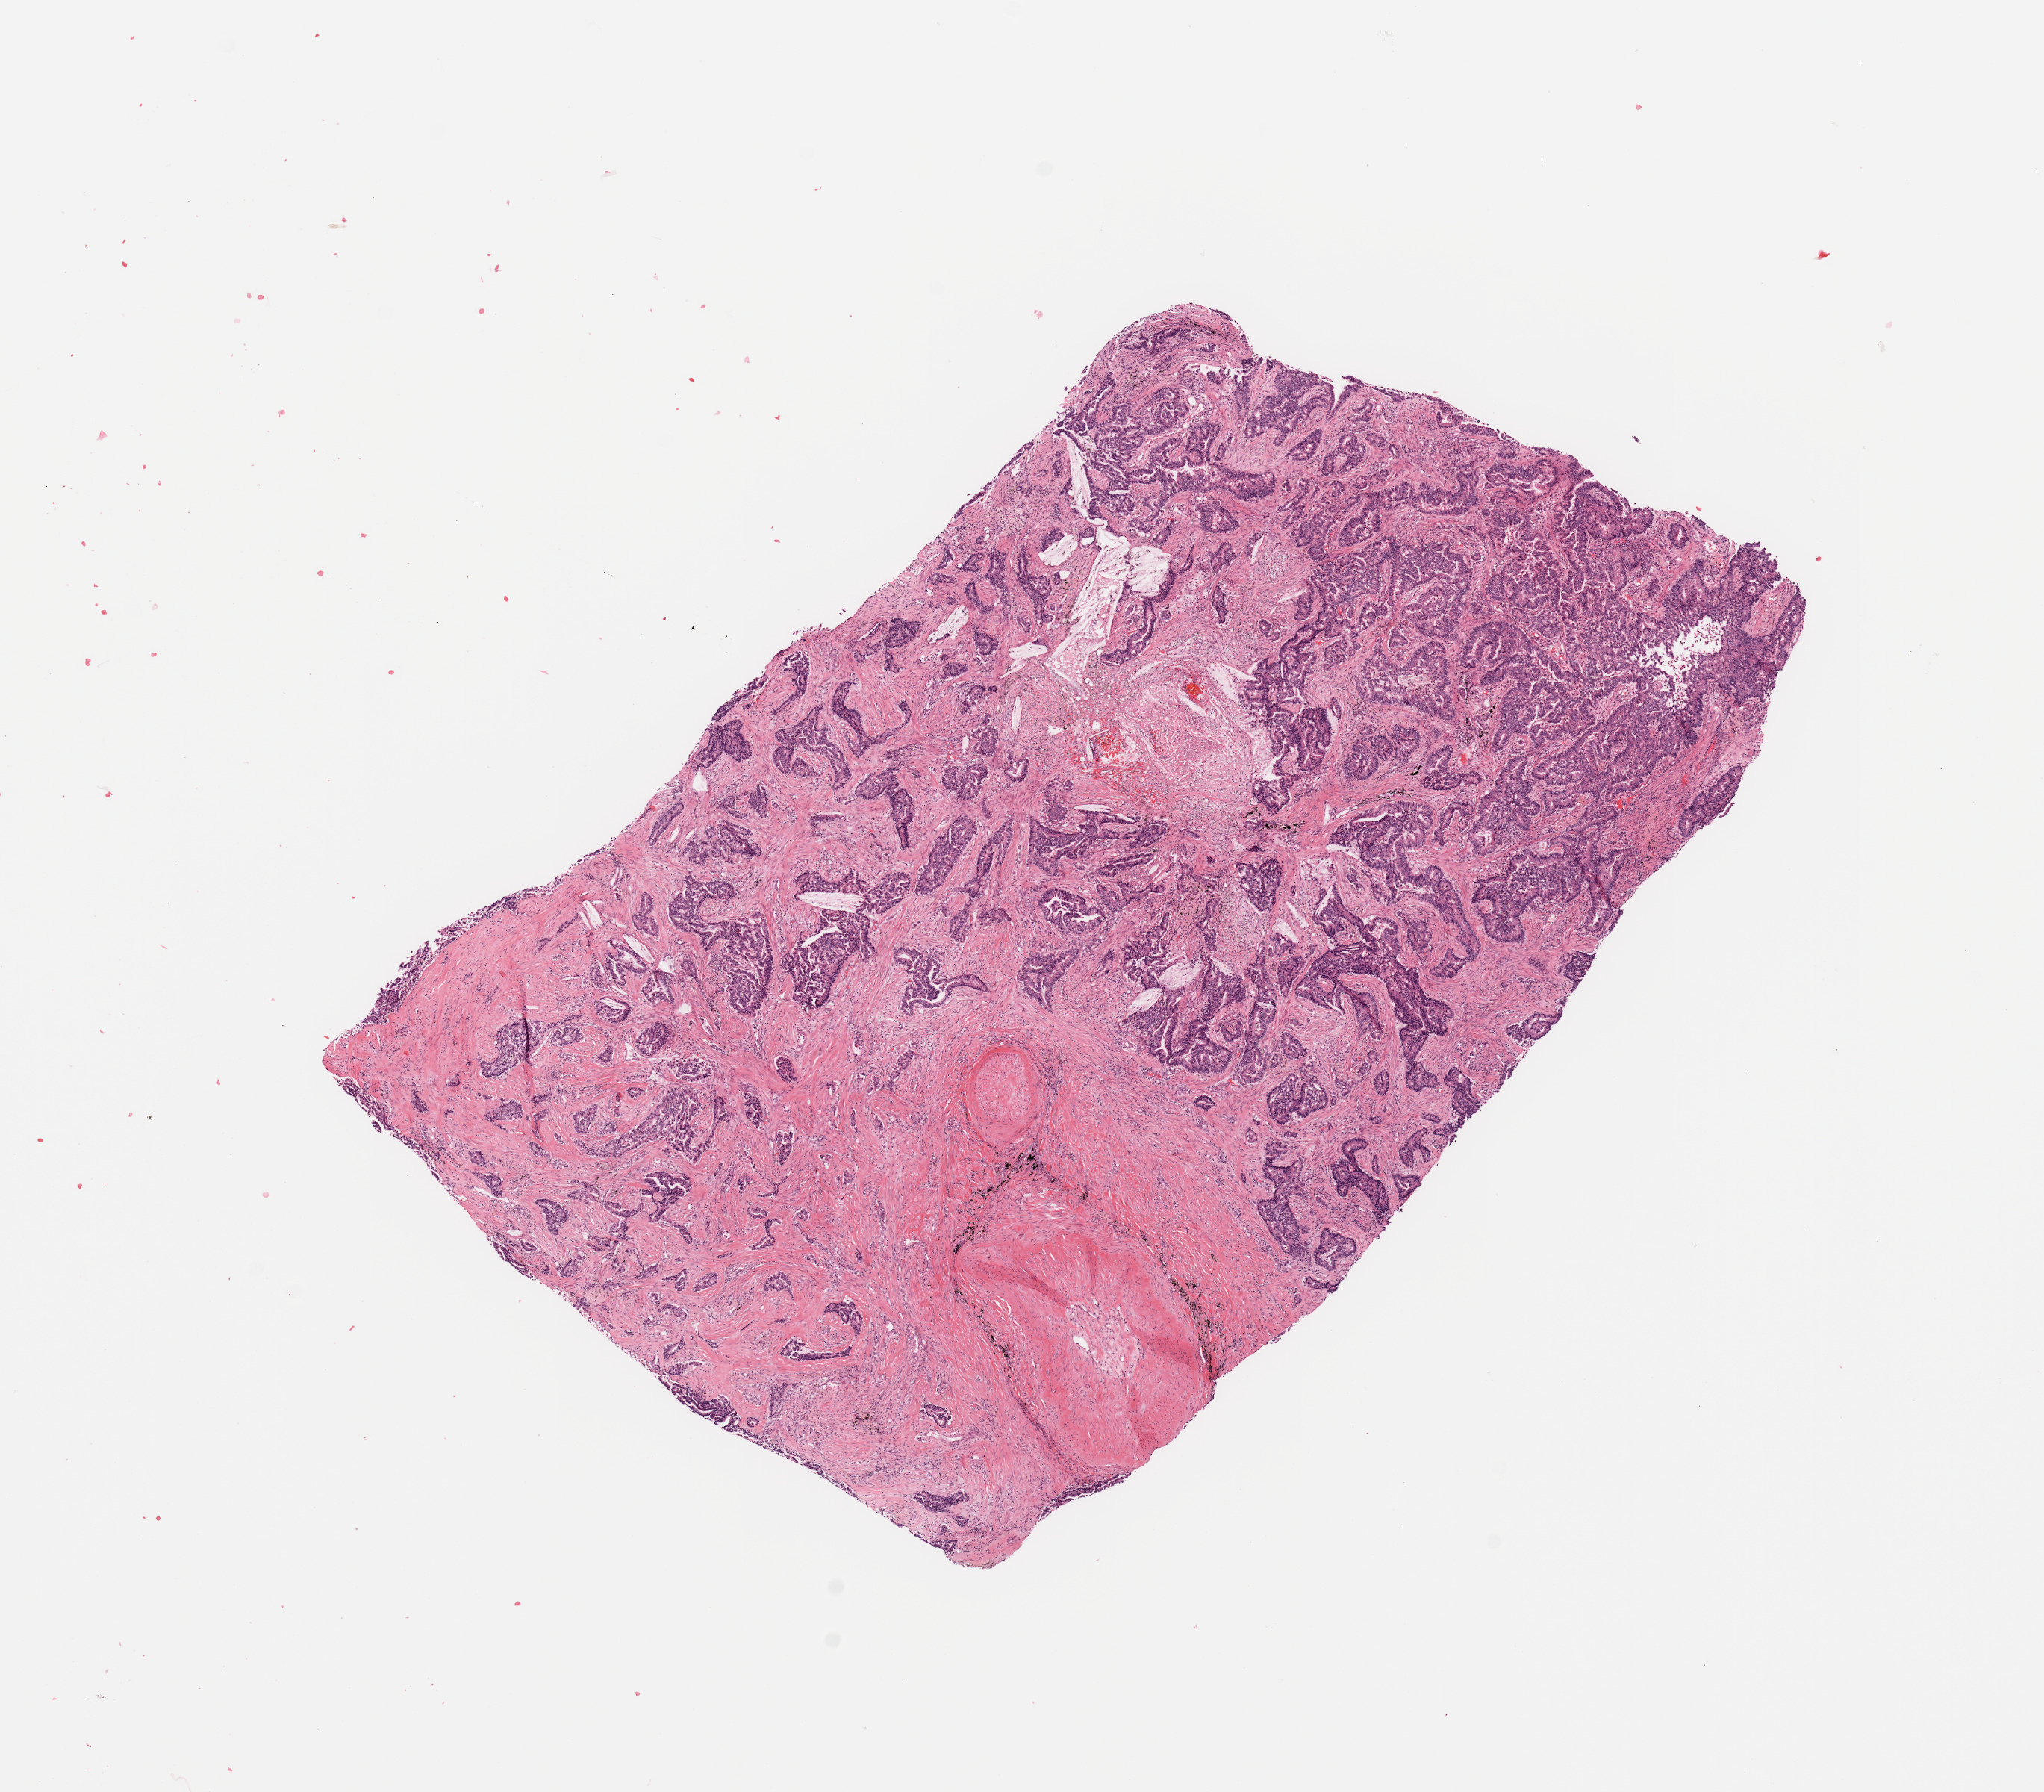
H&E-stained whole-slide image, a low-resolution overview of the entire scanned area, about 10.8 x 9.5 mm (from a 20x scan), tumour tissue sample, lung. 59-year-old female patient. Histologic grade: G2 (moderately differentiated).
• histologic diagnosis: Adenocarcinoma, NOS
• primary tumour site (as recorded): left upper lobe
• AJCC pathologic stage: IB